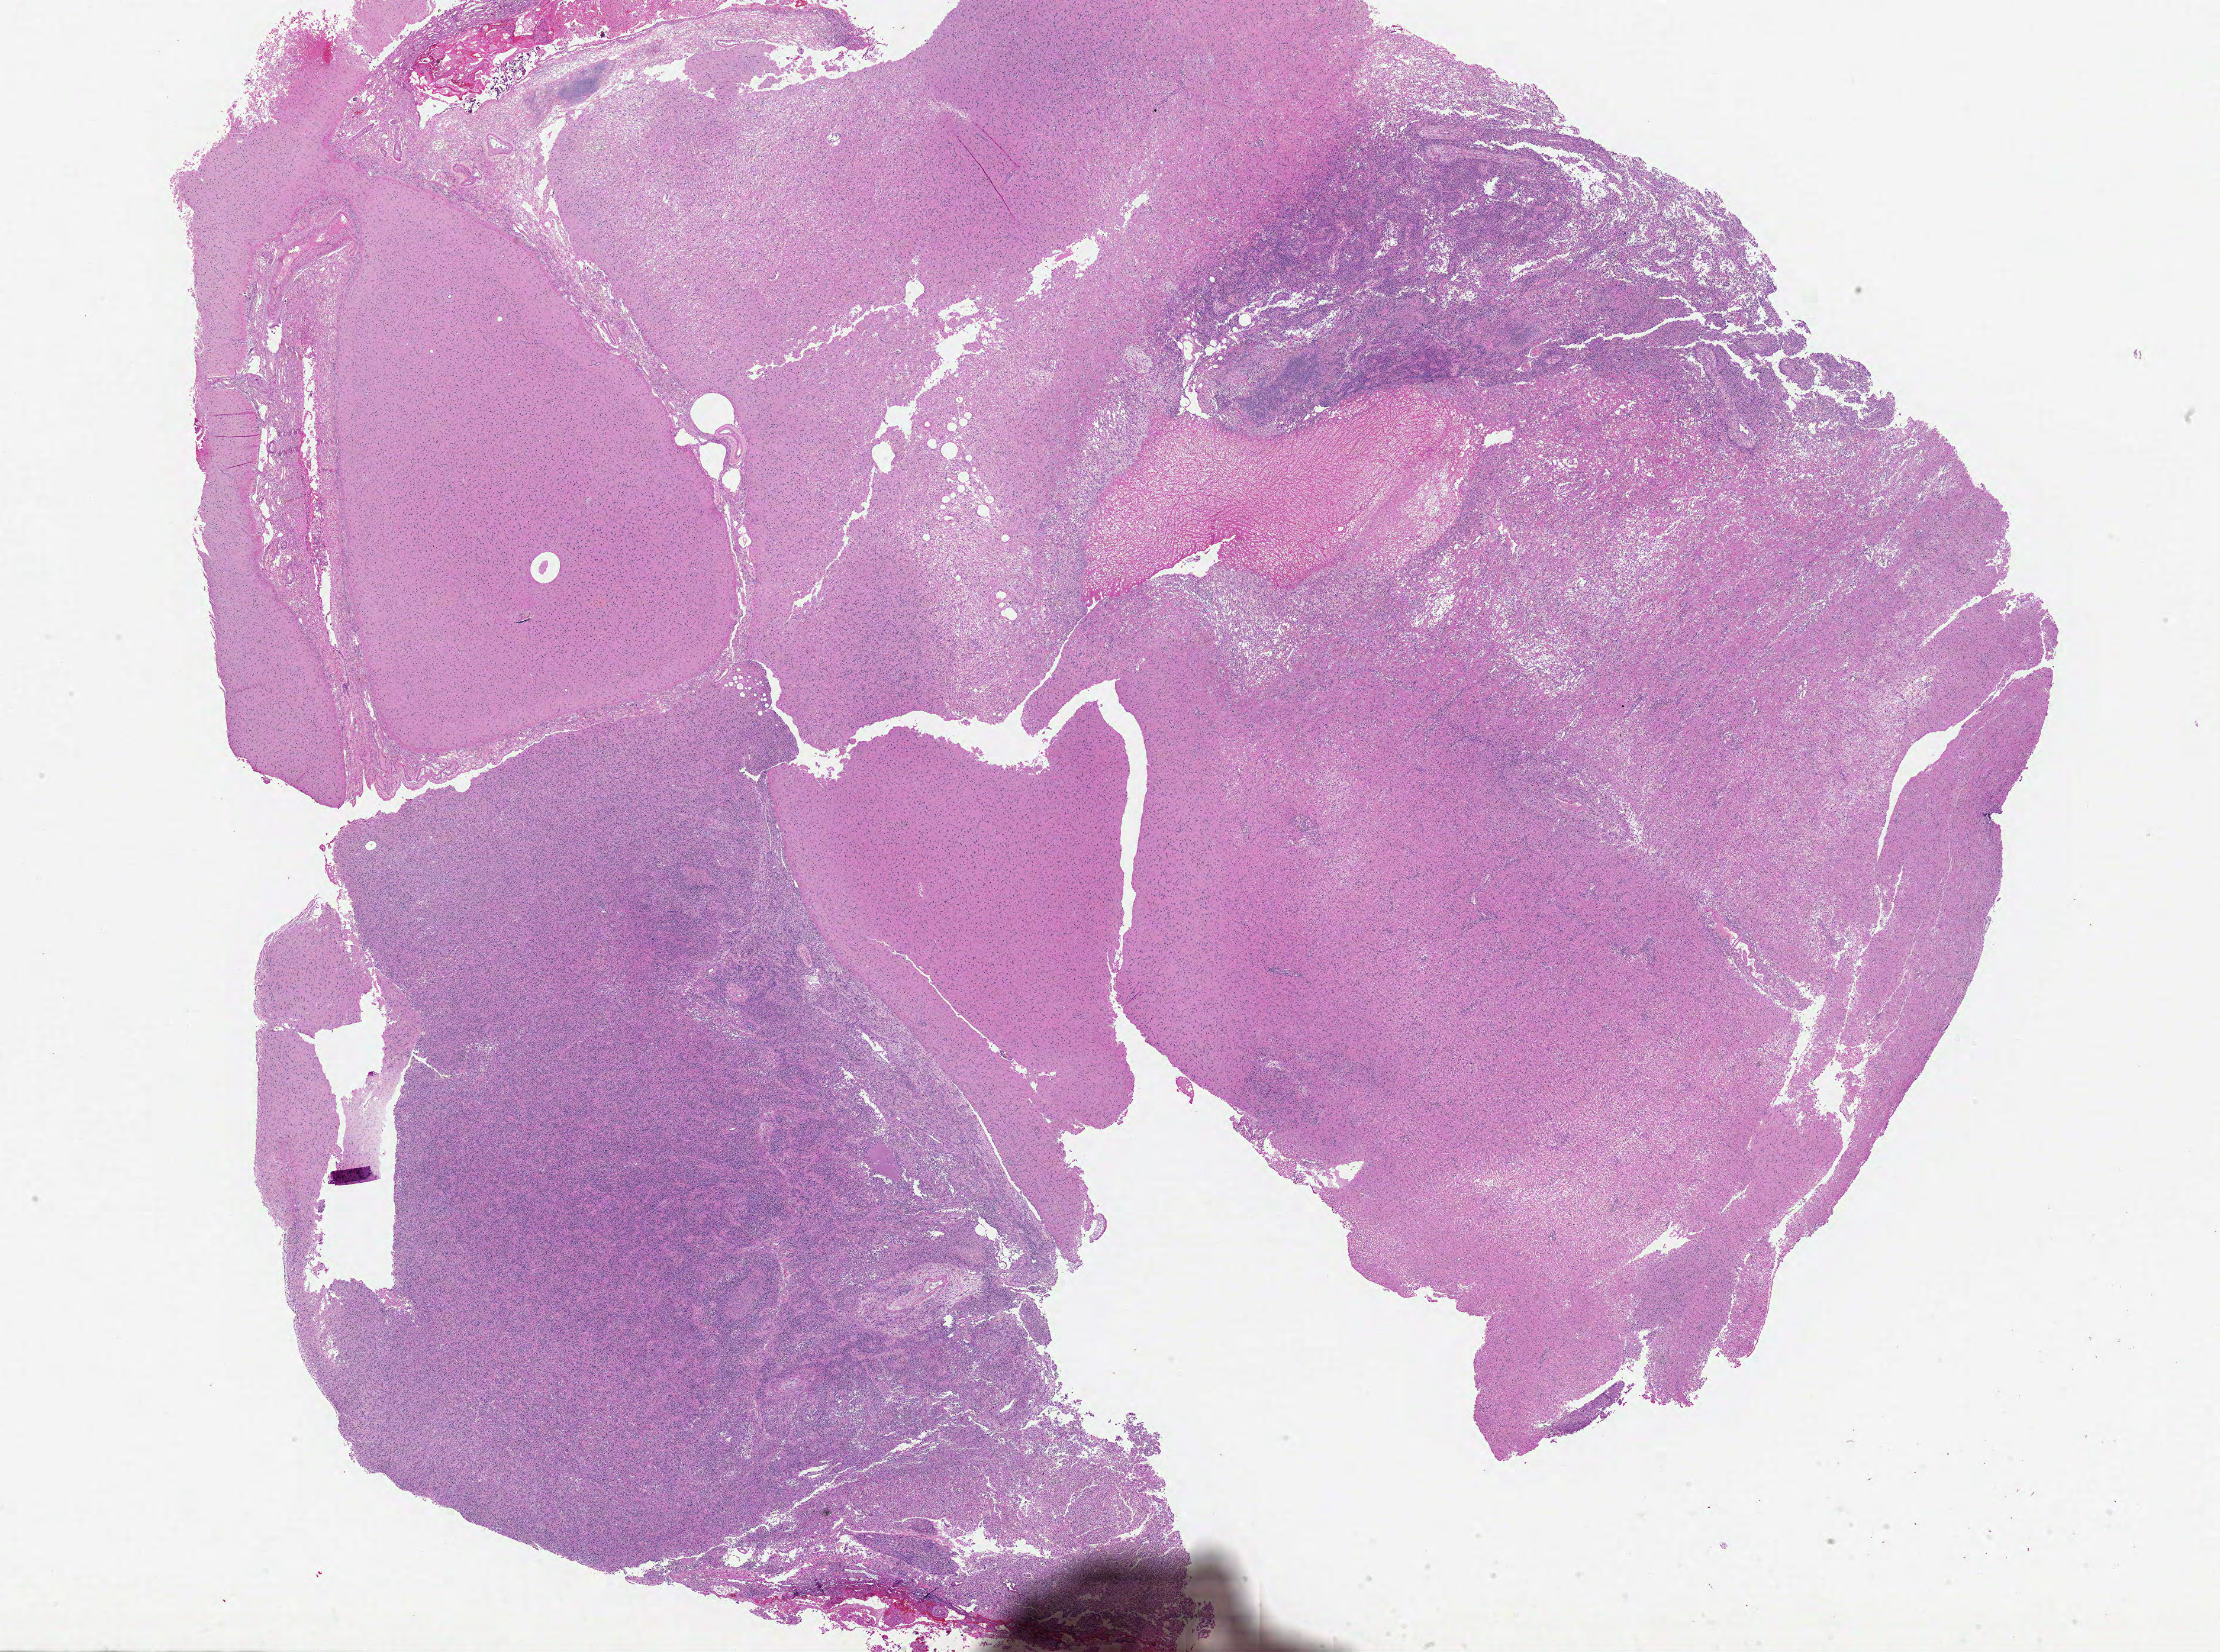
Digitized H&E-stained tissue section (whole slide) — shown as a low-resolution overview of the whole scanned area (about 30.0 x 22.3 mm). Formalin-fixed paraffin-embedded (FFPE) diagnostic section. Sample: primary tumour, brain. Female, age 65 years at initial diagnosis.
- diagnosis: Glioblastoma